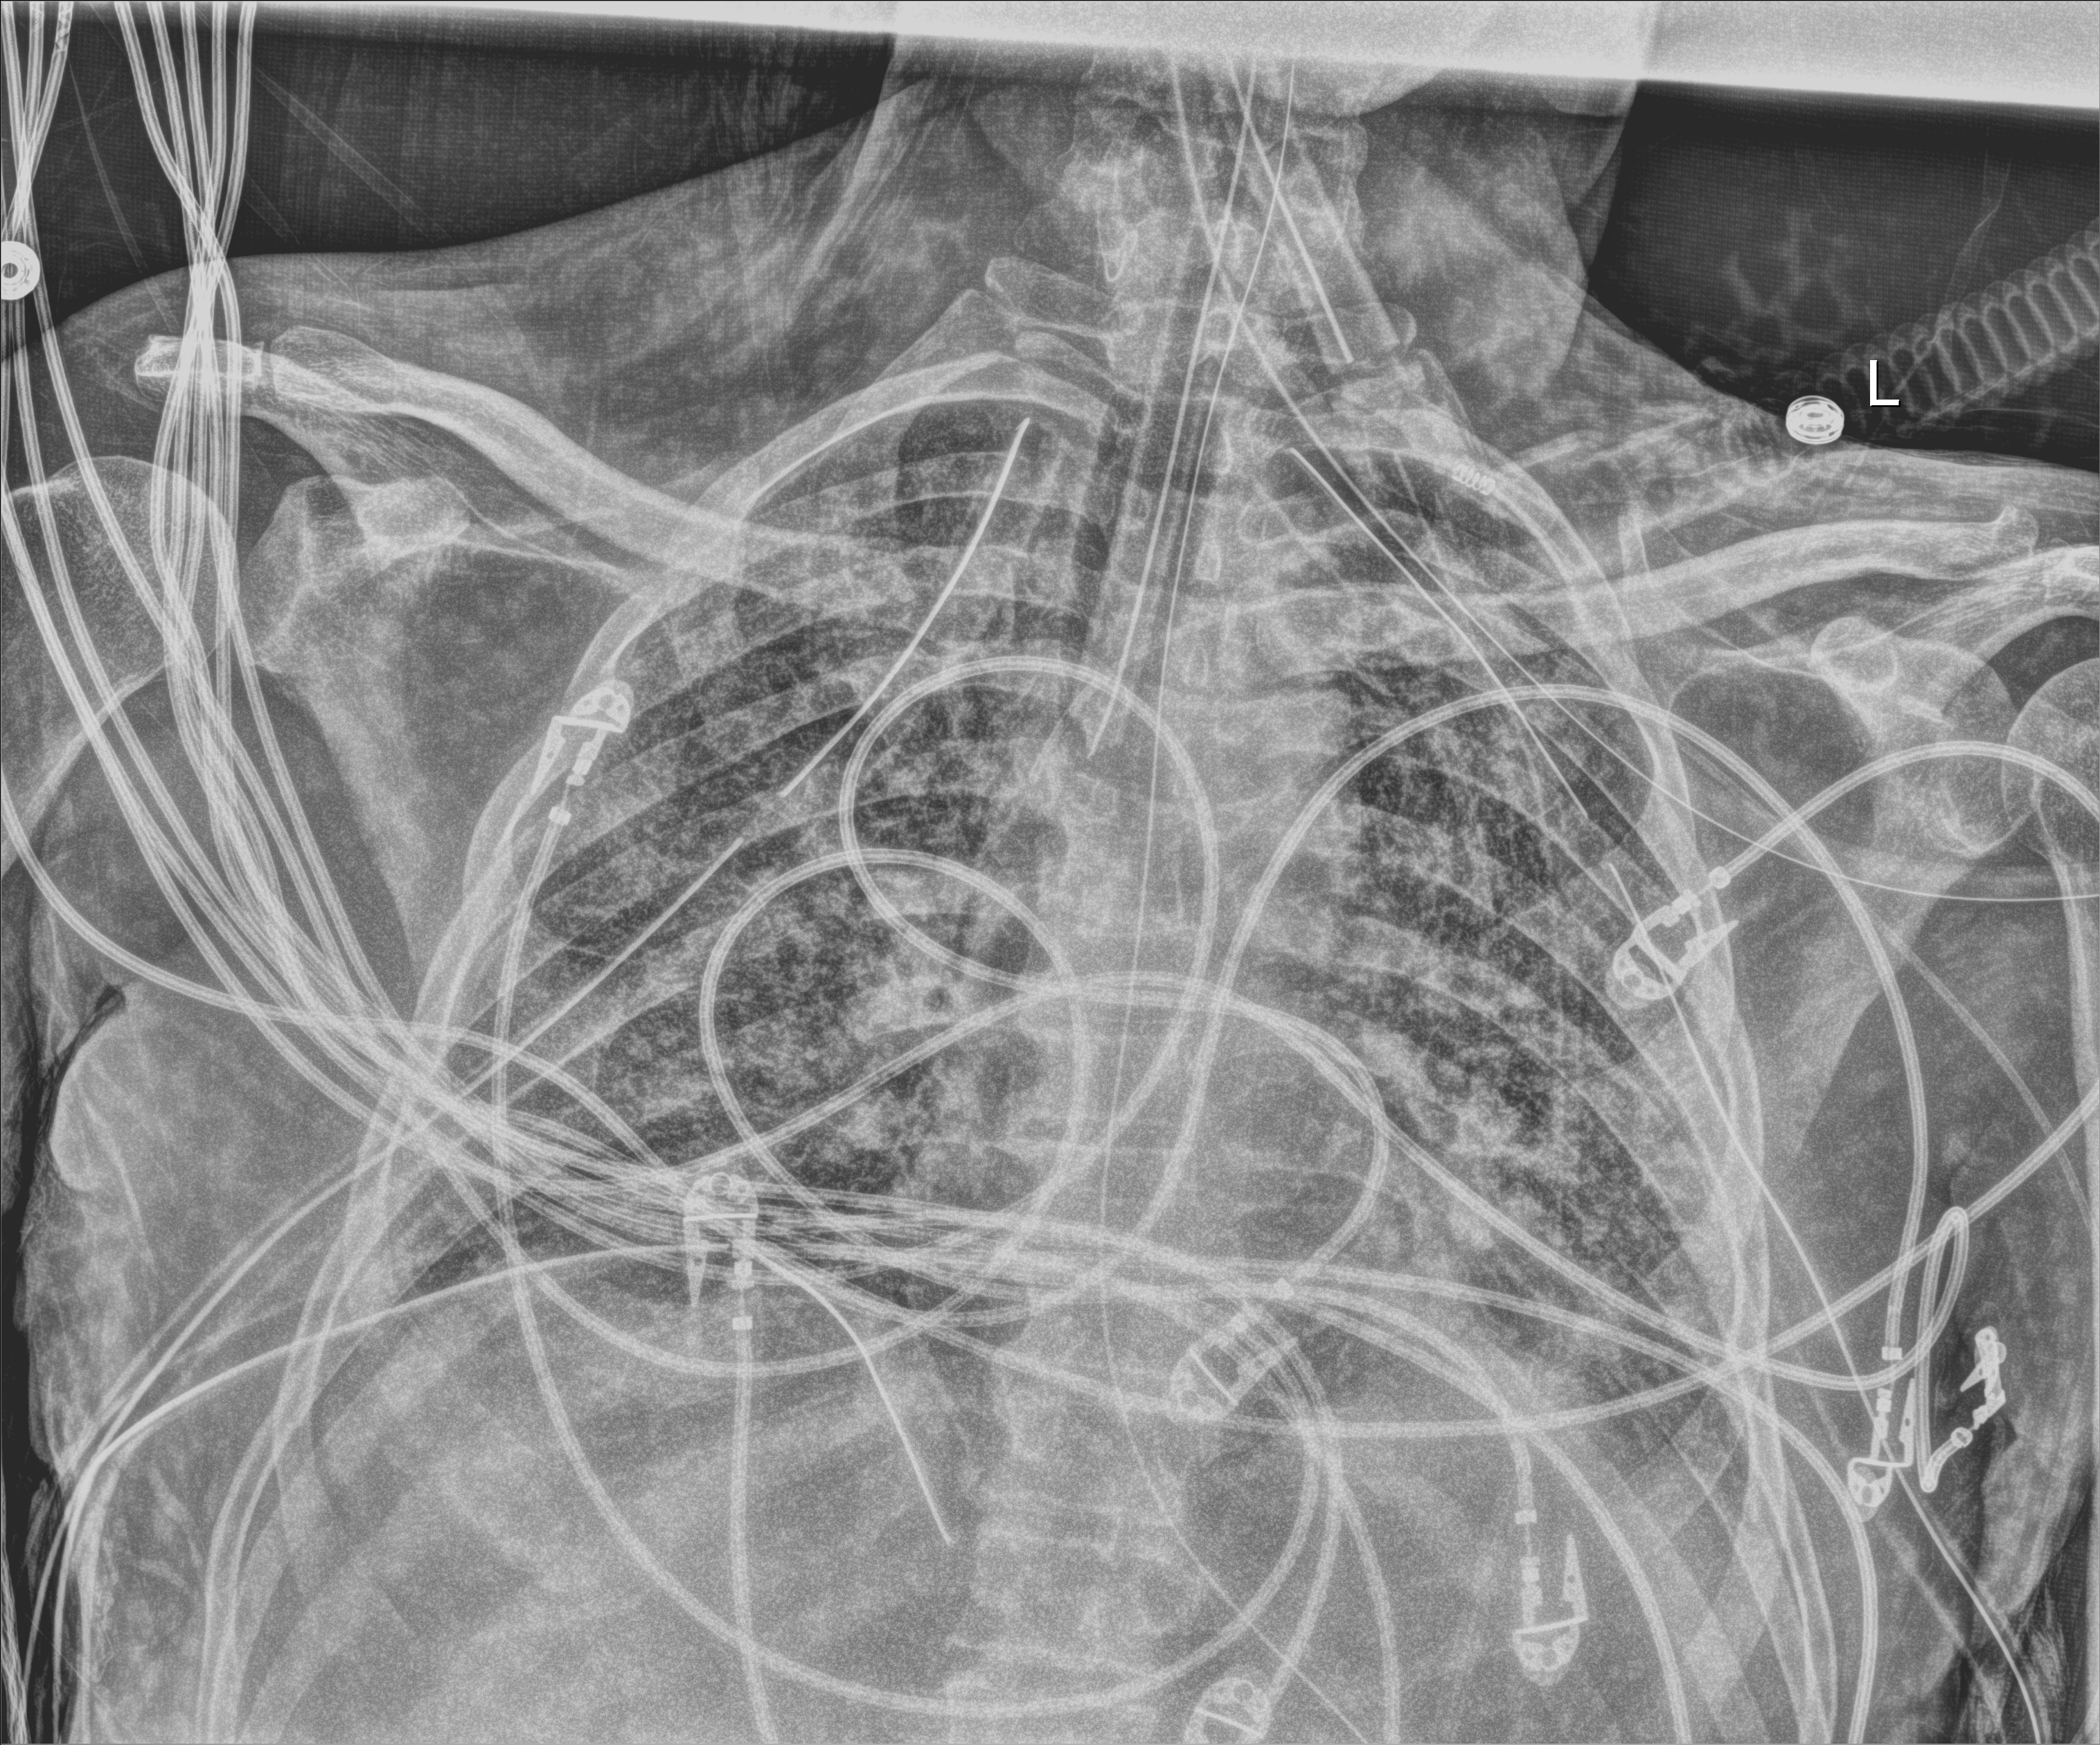
Portable chest radiograph; anteroposterior (AP) projection. Patient hospitalised with COVID-19; male, aged 18–59 years.
From the hospital-stay record, not from the radiograph (when in the stay this image was taken is not recorded): mechanically ventilated during this hospital stay: yes; admitted to intensive care during this hospital stay: yes; COPD (admission record): no.